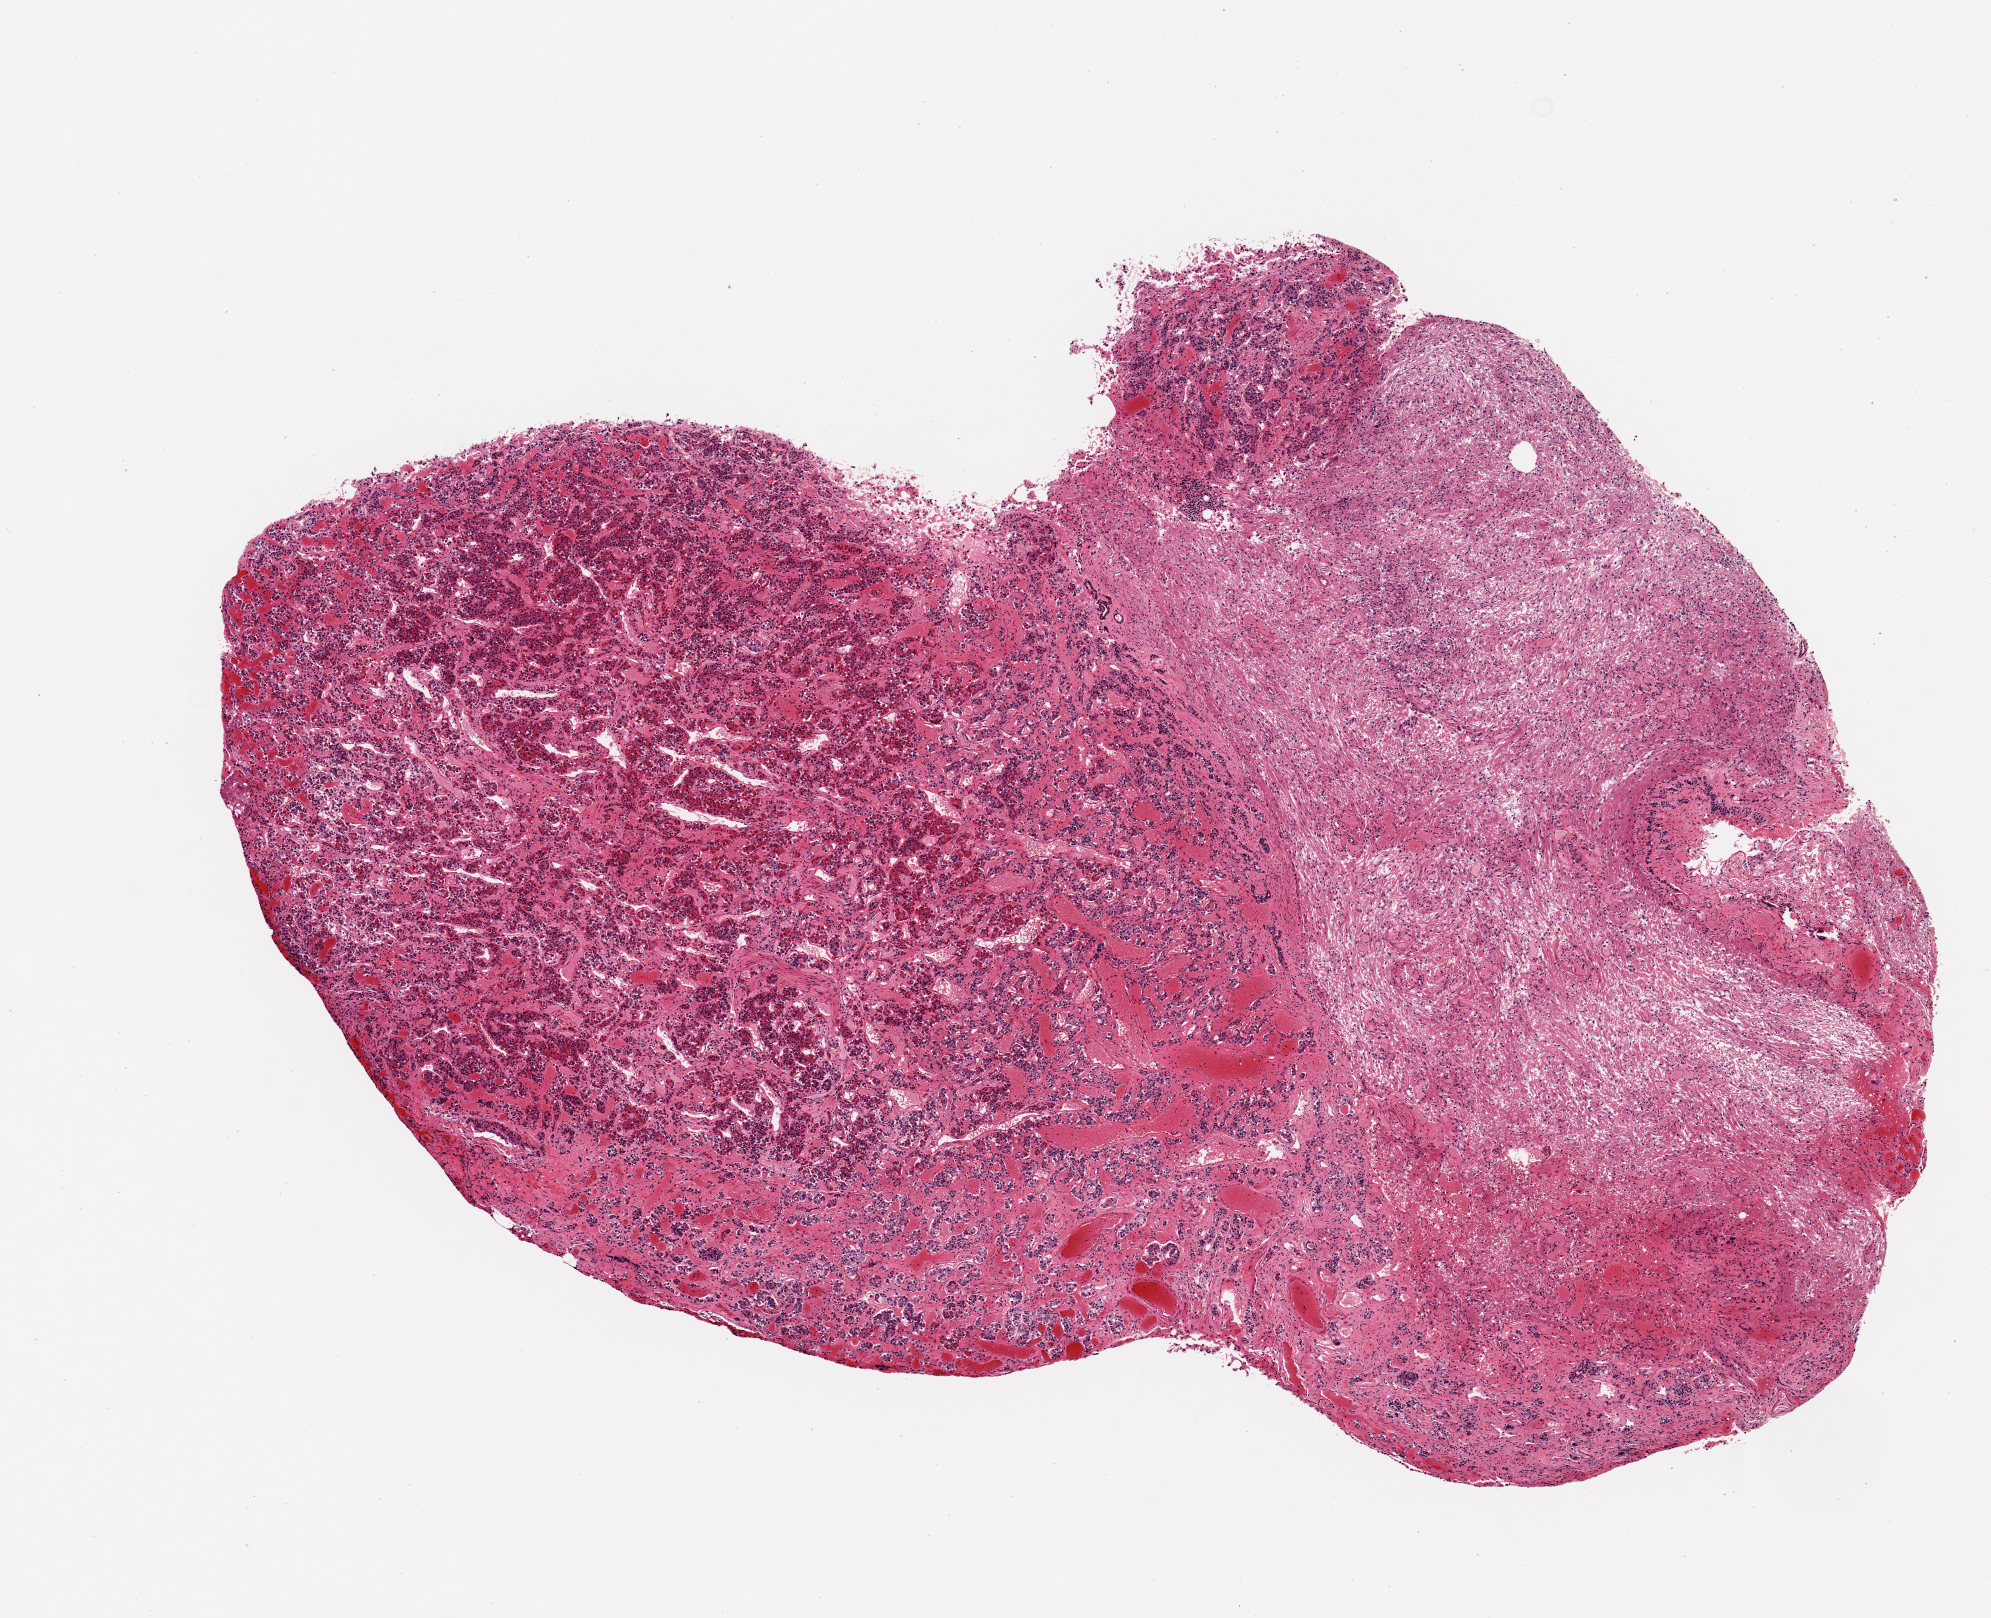
Whole-slide image, H&E stain, brightfield — shown as a low-resolution overview of the whole scanned area (about 7.9 x 6.4 mm). PAXgene-fixed, paraffin-embedded tissue. Section of pituitary (target tissue). Donor tissue sample. Donor: male.
Pathologist's review note for this sample: 1 piece, ~40% neurohypophysis, rest is adenohypophysis.